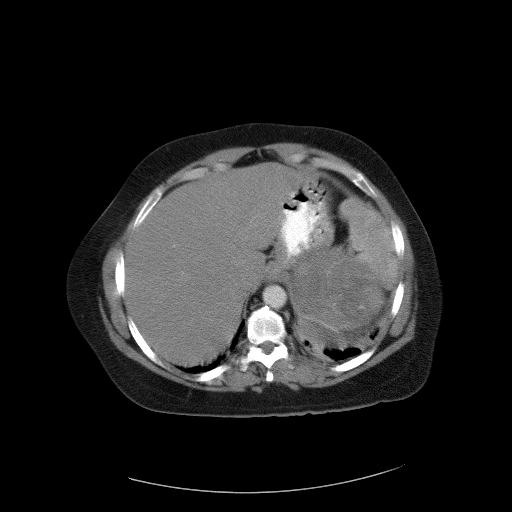
Contrast-enhanced abdominal CT, one axial slice. Position 83 of 90 along the scan axis. Reconstruction kernel FC01. 120 kVp. Soft-tissue window (W 400 / L 40 HU). 5 mm slice thickness. 512 × 512 image matrix, field of view 480 × 480 mm. Female patient, age 55 years. From the clinical record (not read from this slice): diagnosis: adrenocortical carcinoma; tumour side: left adrenal; tumour size at pathology: 22 cm; Ki-67 index: 10 %; stage (as recorded): 3.
Annotated regions visible in this slice (semi-automatic segmentation, software-assisted and operator-edited):
- mass: bounding box (x1, y1, x2, y2) in pixels: (291, 251, 382, 327)